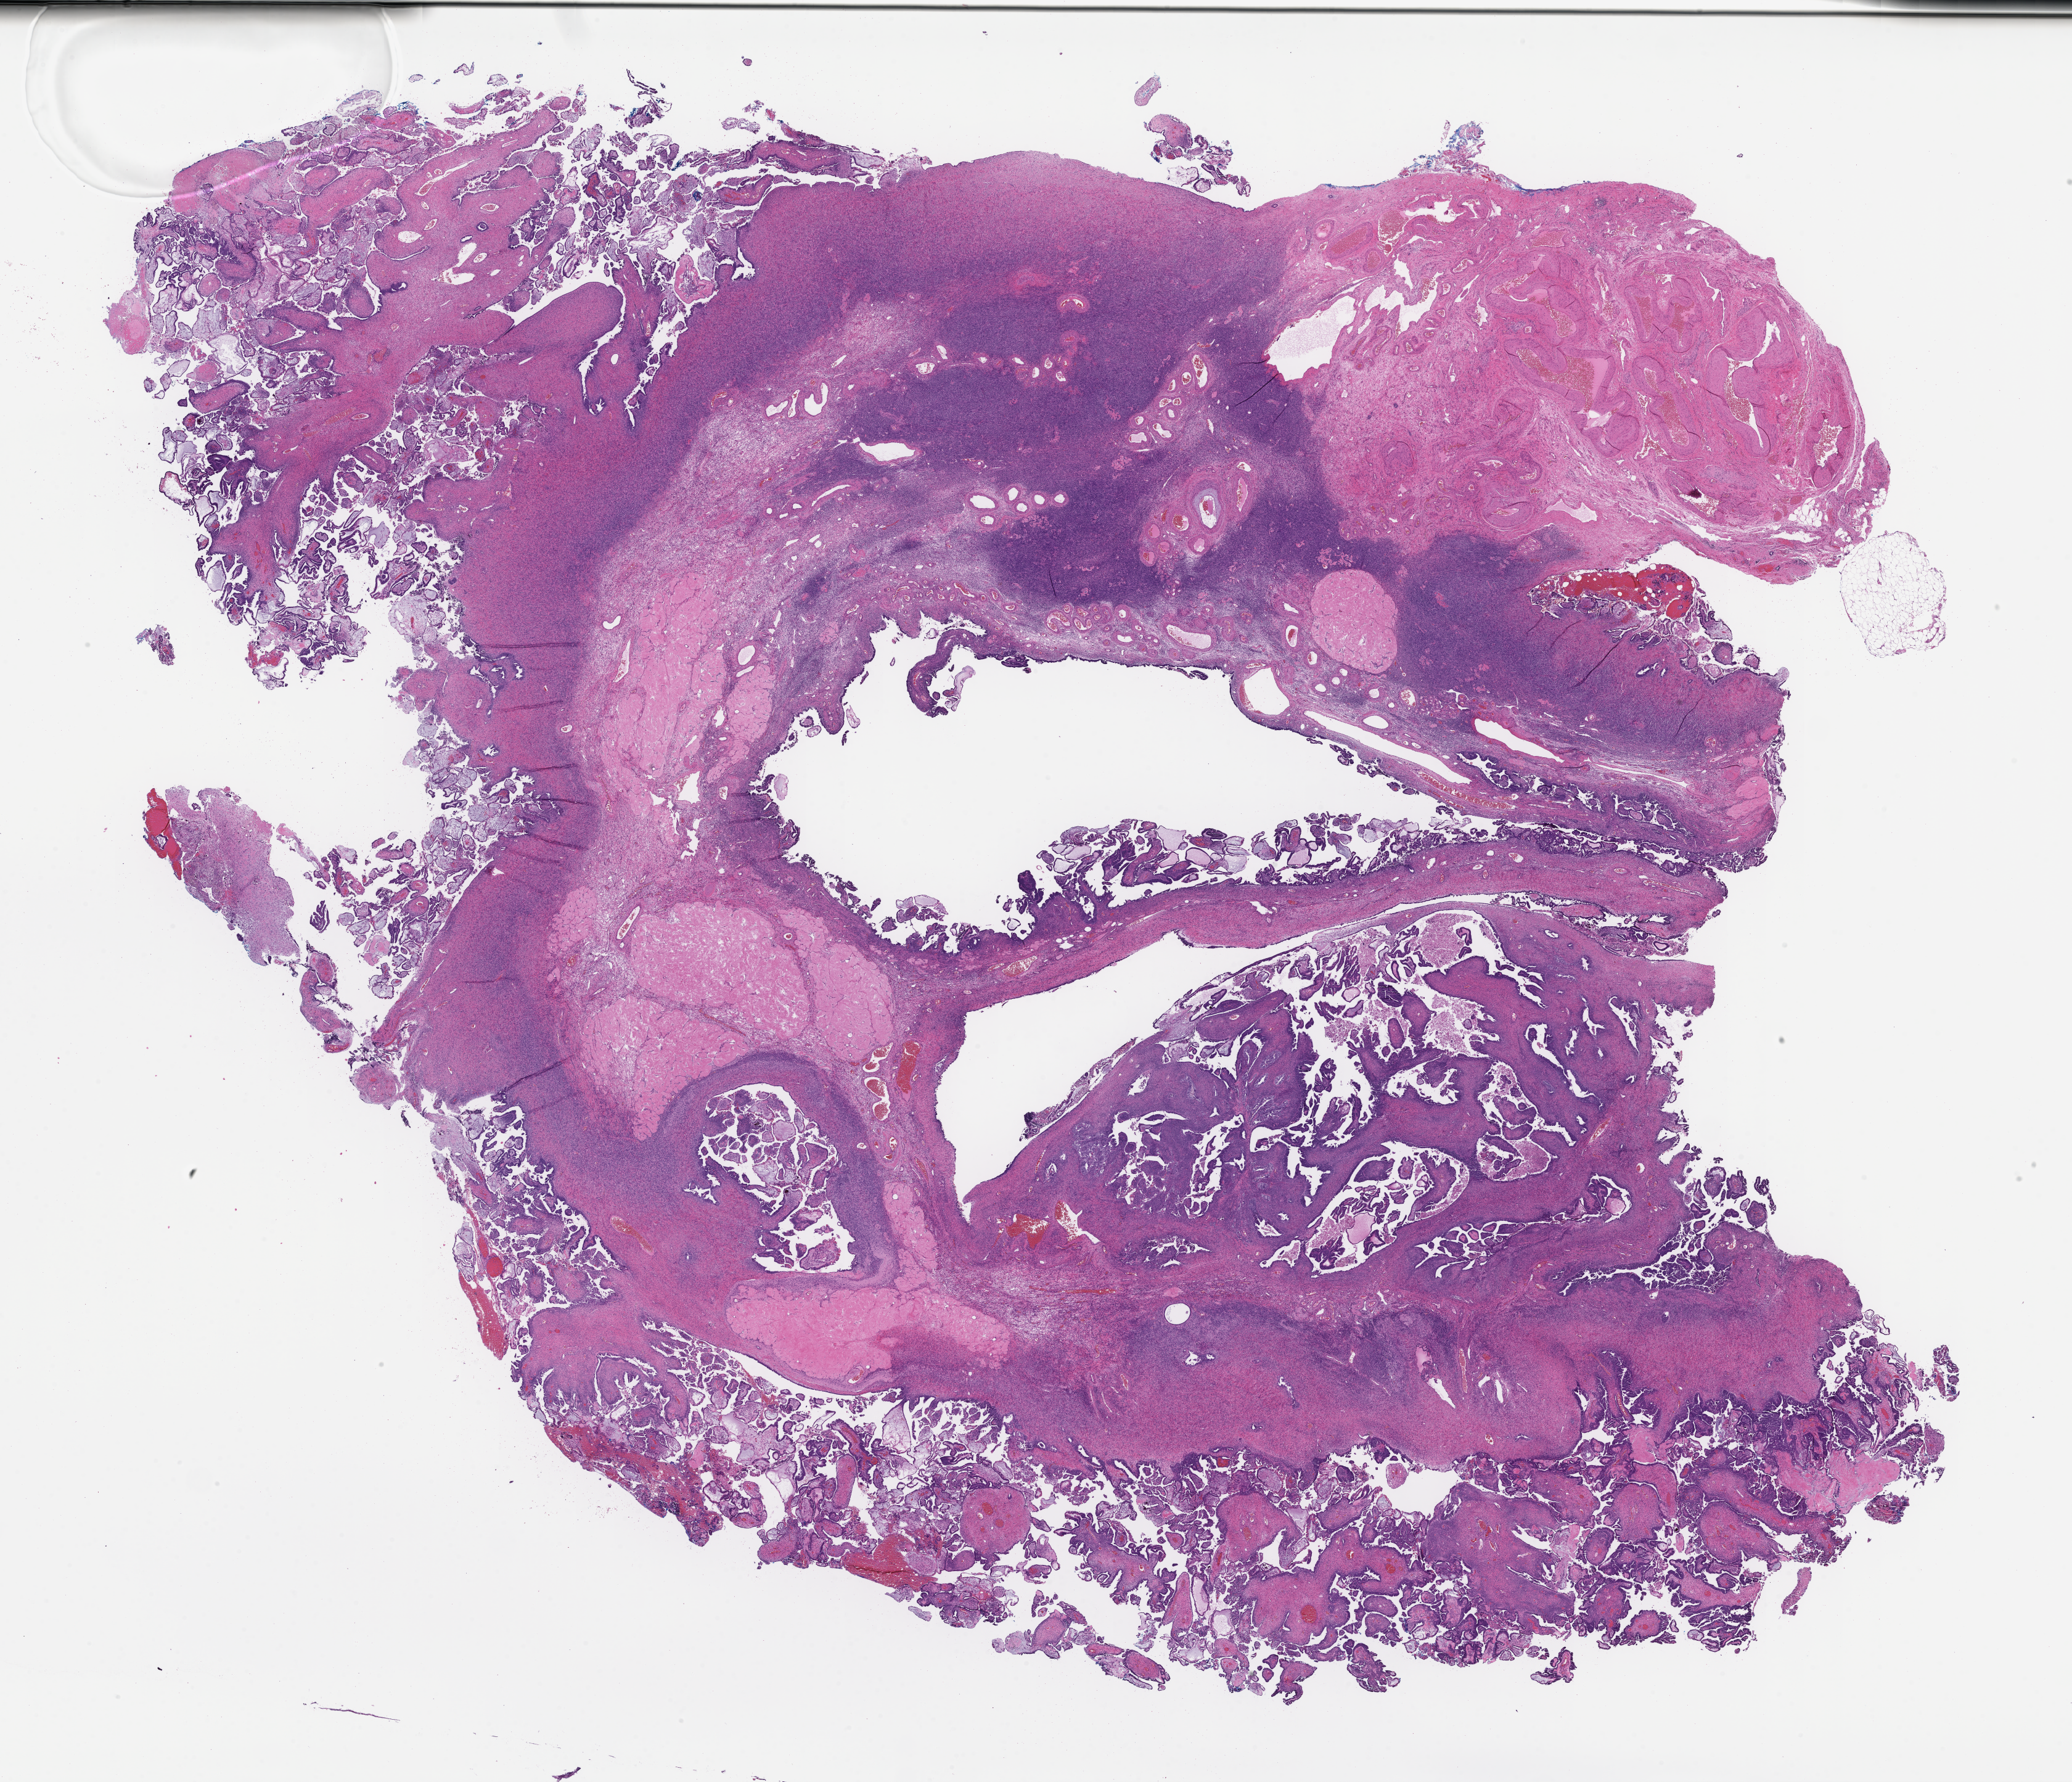
Whole-slide image, H&E stain, shown as a low-resolution overview of the whole scanned area (about 27.1 x 23.3 mm). Formalin-fixed, paraffin-embedded (FFPE) tissue. Tissue site: ovary. Collected on treatment. Female patient.
This section: primary tumor. Diagnosis: Ovarian Carcinoma.